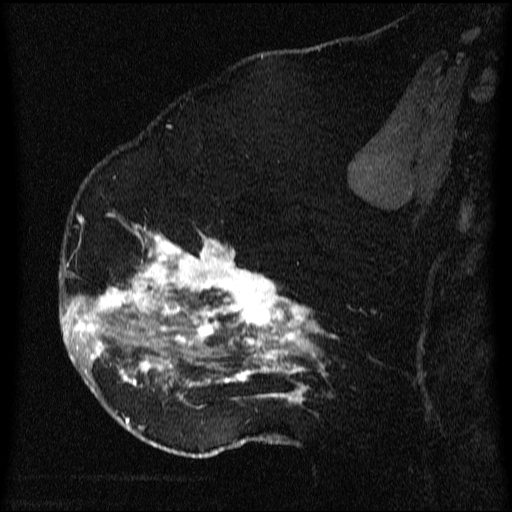
Breast MRI (dynamic contrast-enhanced), one sagittal slice; position 39 of 64 along the scan axis; dynamic contrast-enhanced series, image 2 of 3 at this slice position (ordered by acquisition); 1.5 T; TE 4.2 ms, TR 9.1 ms; 2.2 mm slice thickness; 512 × 512 image matrix, field of view 180 × 180 mm. Female patient, age 52 years.
Outlined on this slice (semi-automatic segmentation, software-assisted and operator-edited):
- analysis volume of interest (the breast-tissue region the enhancement analysis was run in; not a lesion): bounding box (x1, y1, x2, y2) in pixels: (61, 203, 346, 438)
- tumour enhancement mask (voxels above the 70 % enhancement threshold inside the analysis volume of interest): (61, 222, 331, 428)